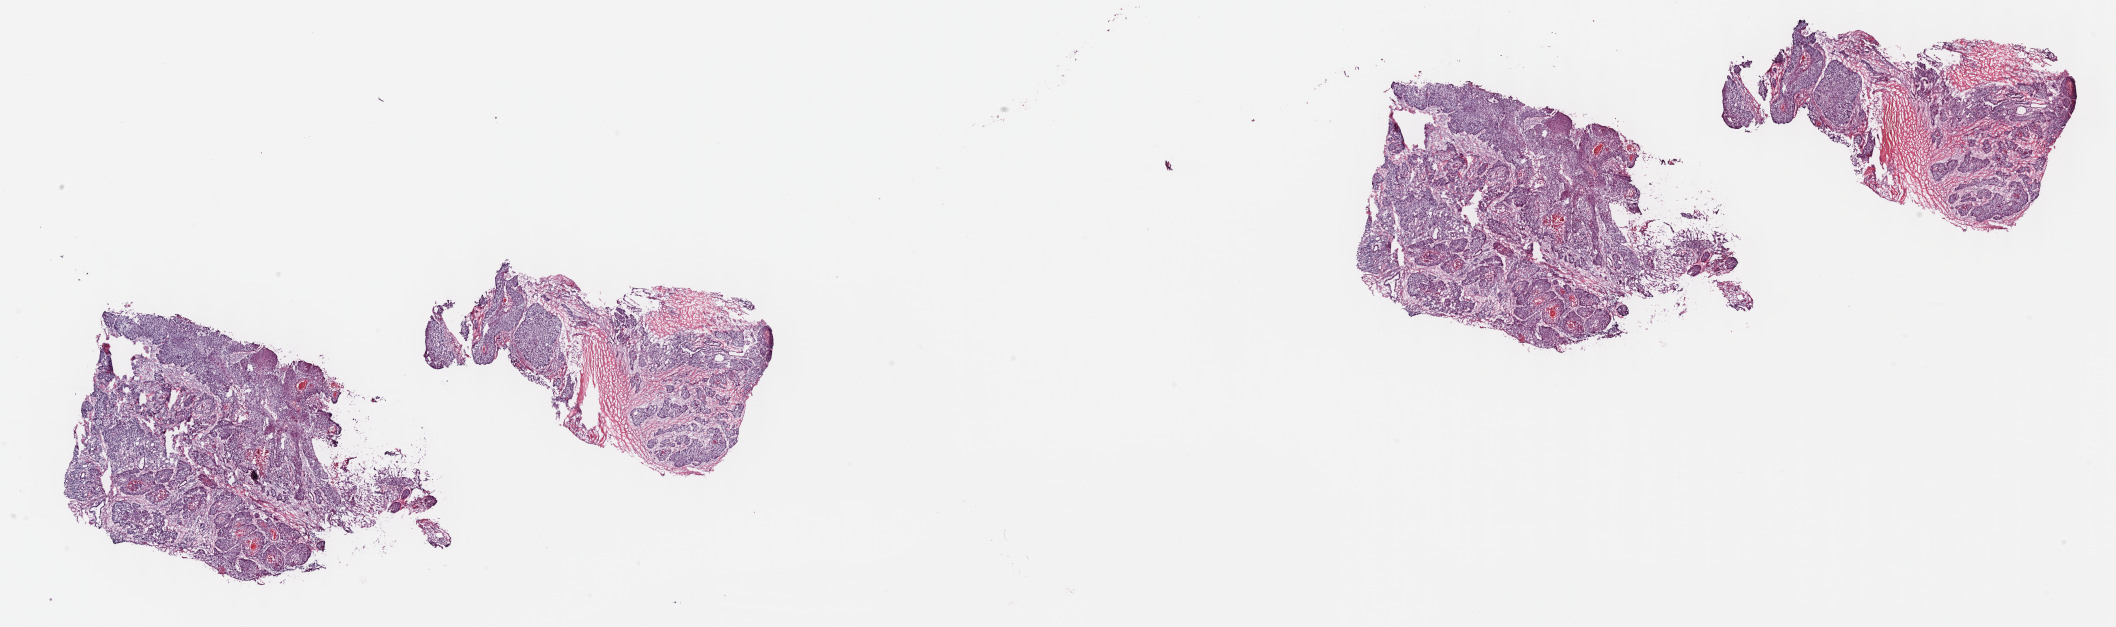
Digitized Hematoxylin and eosin (H&E) stained tissue section (whole slide) — low-resolution overview of the scanned area, about 34.2 x 10.1 mm, frozen section from the top of the tissue portion, head and neck, primary tumour sample. Patient: male, age at initial diagnosis 80 years. Histologic grade: G2 (moderately differentiated). Pathologist review of this section (percent, as recorded): tumour cells 65%, tumour nuclei 75%, normal cells 0%, stromal cells 35%, necrosis 0%. Infiltration values recorded for this section: lymphocyte infiltration 0%, monocyte infiltration 0%, neutrophil infiltration 0%.
AJCC pathologic stage: IVA (7th edition). Diagnosis: Squamous cell carcinoma, NOS (larynx, NOS). Laterality: left.